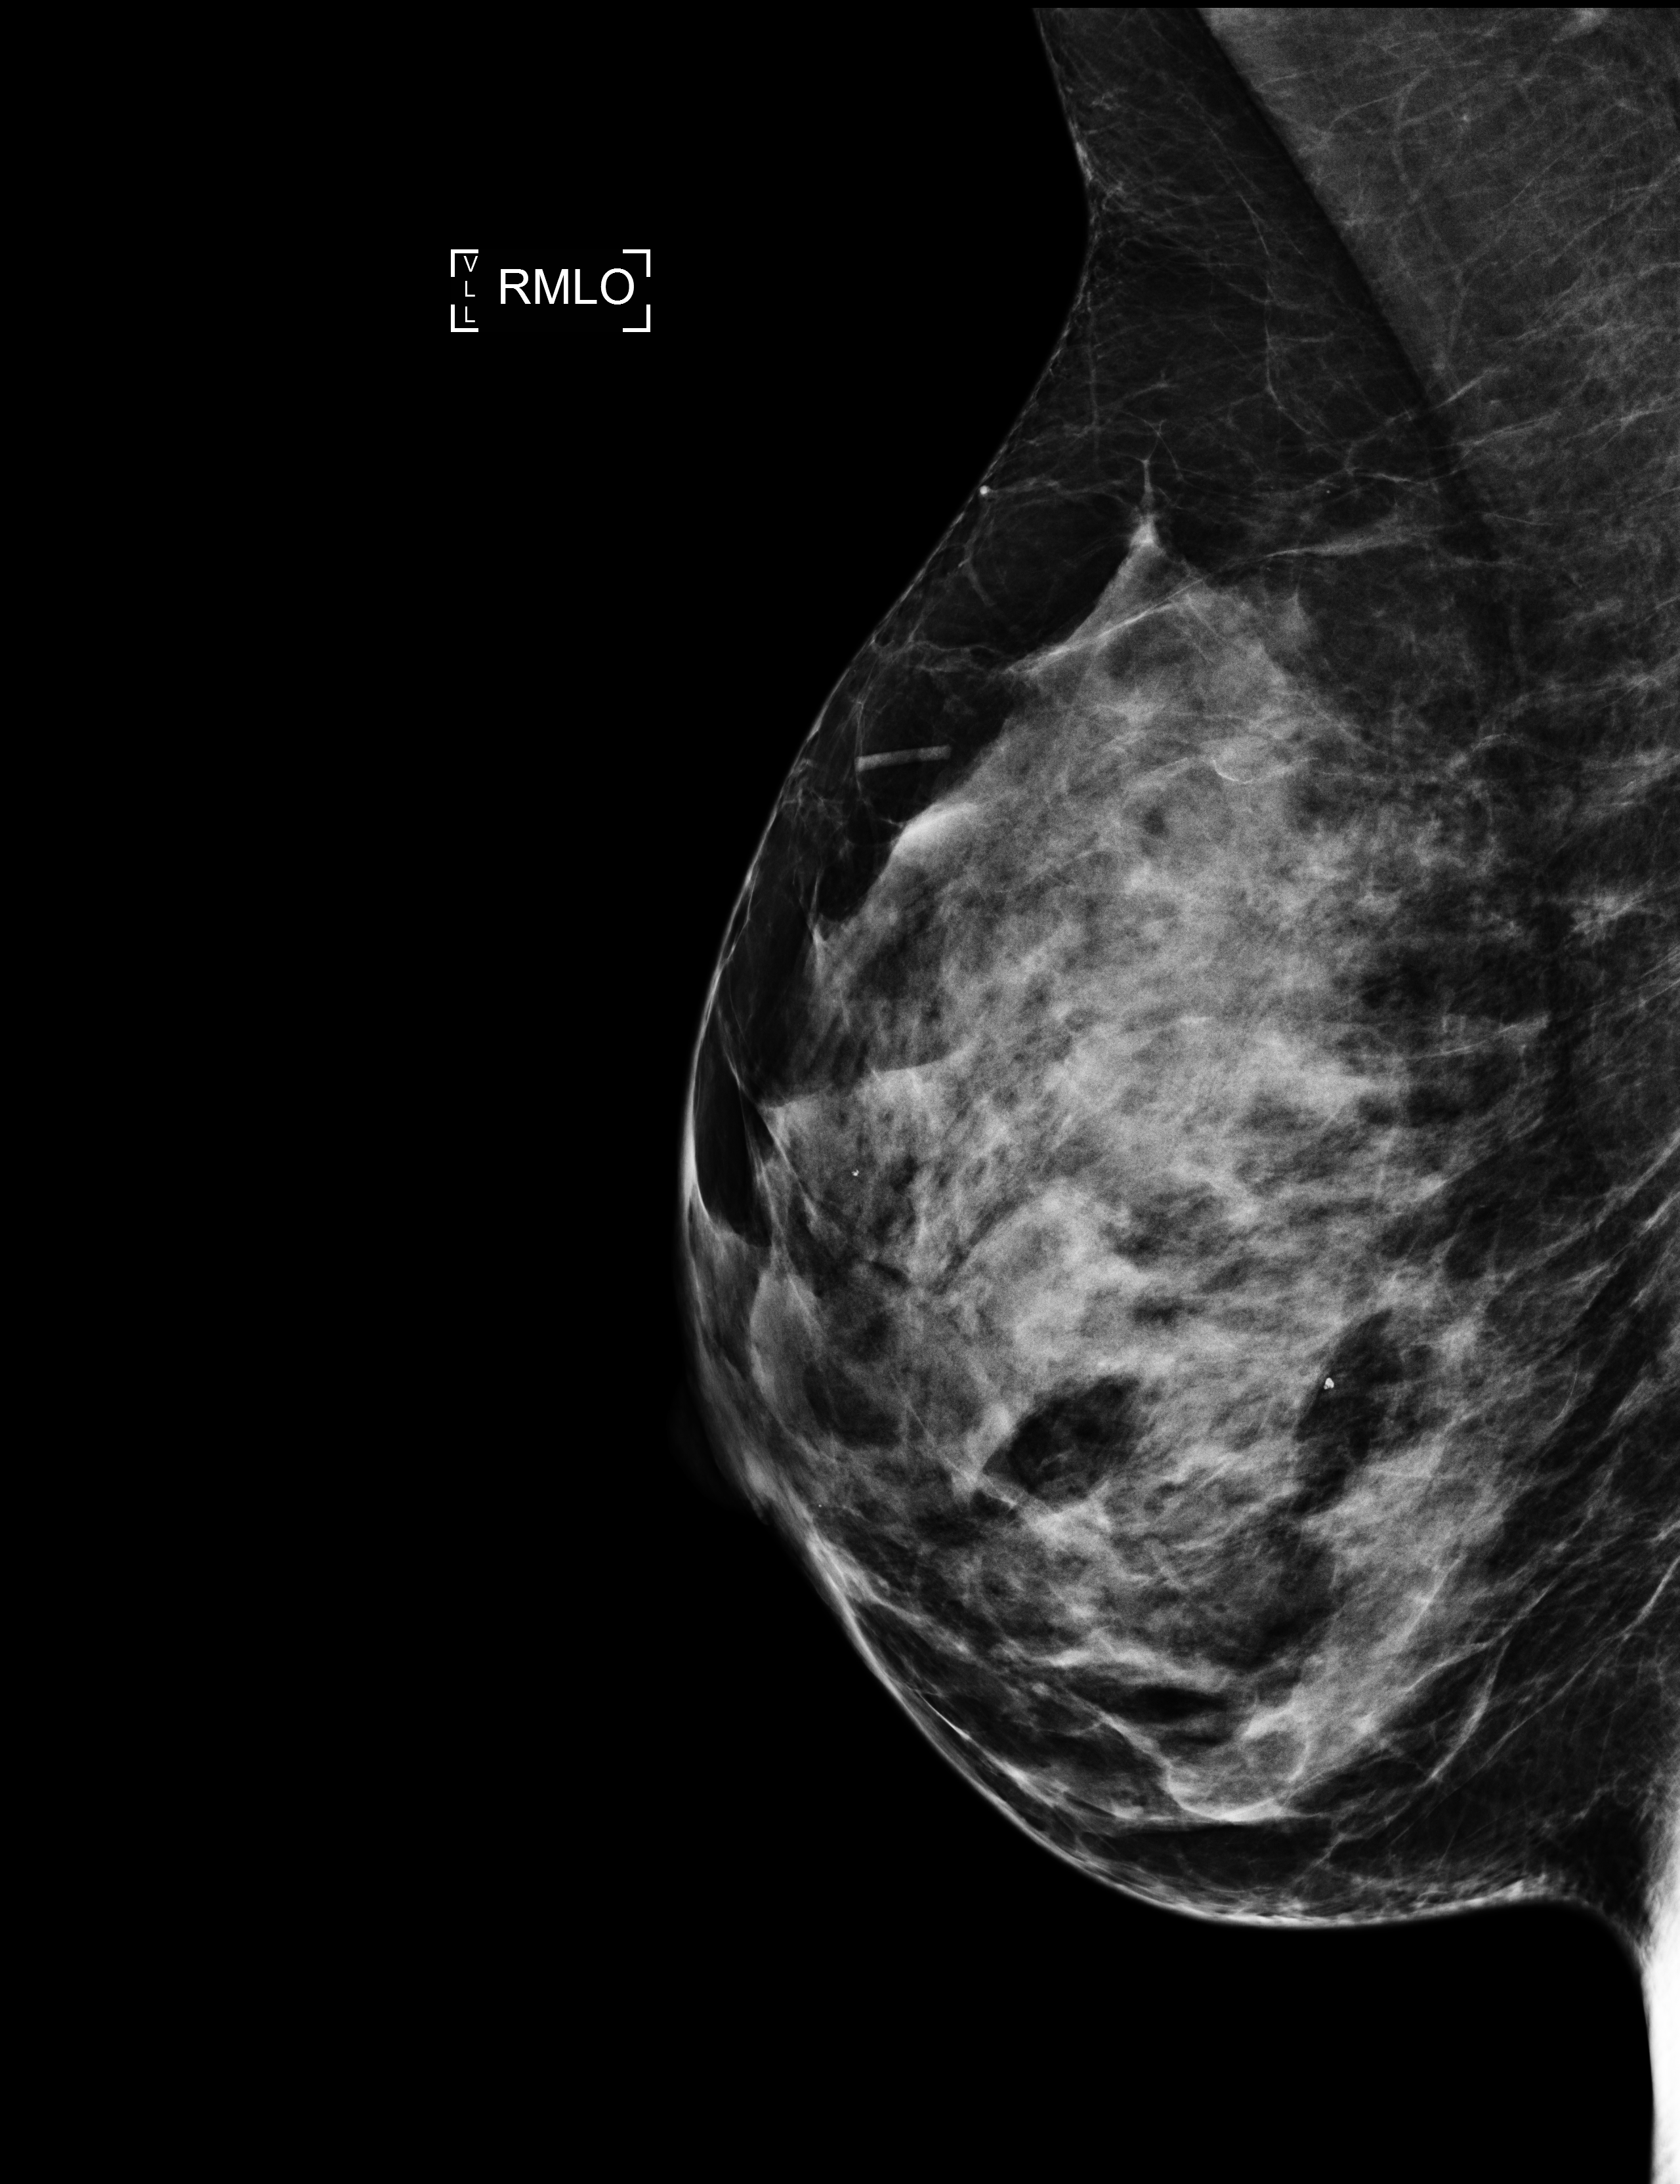
Annual screening mammography examination, compressed breast thickness 60 mm. Patient aged 48 years (female).
Image type: full-field digital mammogram. Breast: right. Projection: MLO view.